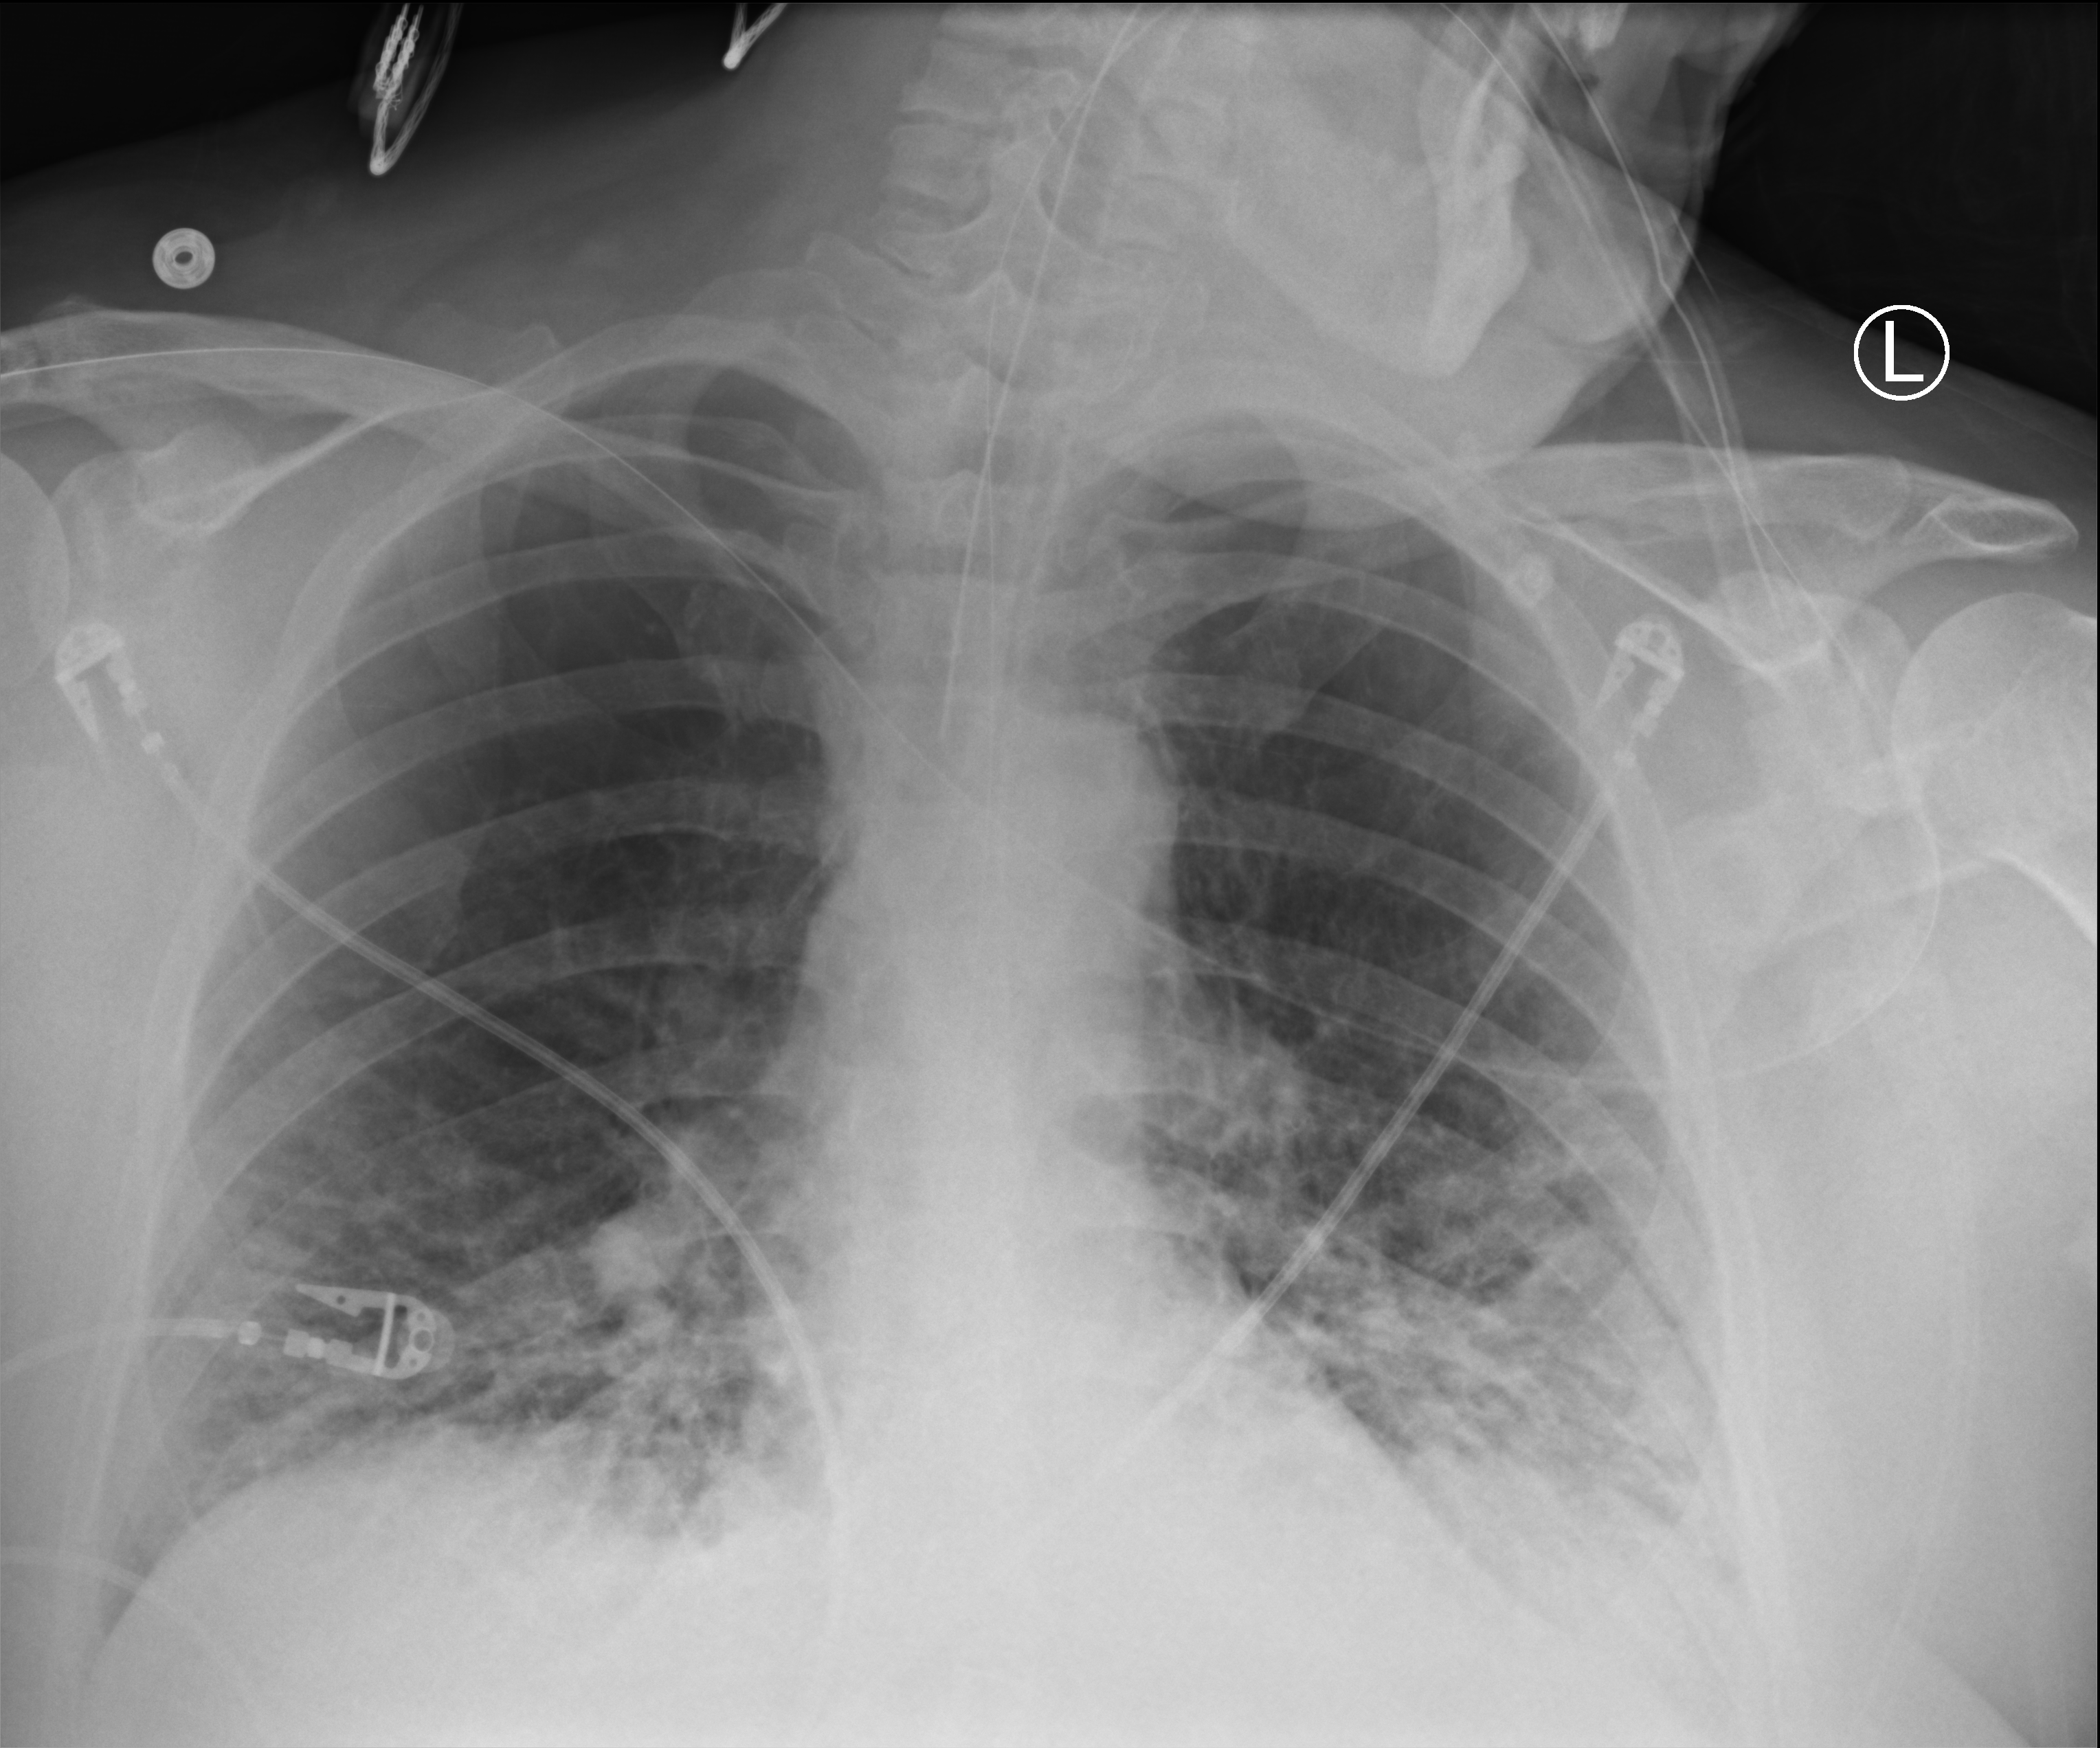
Chest X-ray (portable), anteroposterior (AP) projection. Patient hospitalised with COVID-19, aged 18–59 years.
From the hospital-stay record, not from the radiograph (when in the stay this image was taken is not recorded):
- admitted to intensive care during this hospital stay: yes
- length of hospital stay: 9 days
- mechanically ventilated during this hospital stay: yes